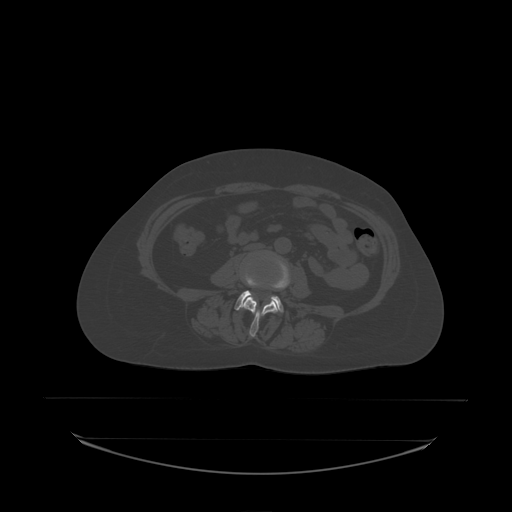
CT including the spine, one axial slice. Slice 56 of 242 in the series (ordered by position). Bone window (W 1800 / L 400 HU). 2.5 mm slice thickness. 512 × 512 image matrix, field of view 500 × 500 mm. Female patient, age 53 years. From the clinical record (not read from this slice): primary cancer: lung; vertebrae with lytic lesions (as recorded): T7, L1.
Outlined on this slice (semi-automatic segmentation, software-assisted and operator-edited):
- L3 vertebra: bounding box <244,263,290,338> (left, top, right, bottom; pixels)
- L4 vertebra: <235,276,284,313>